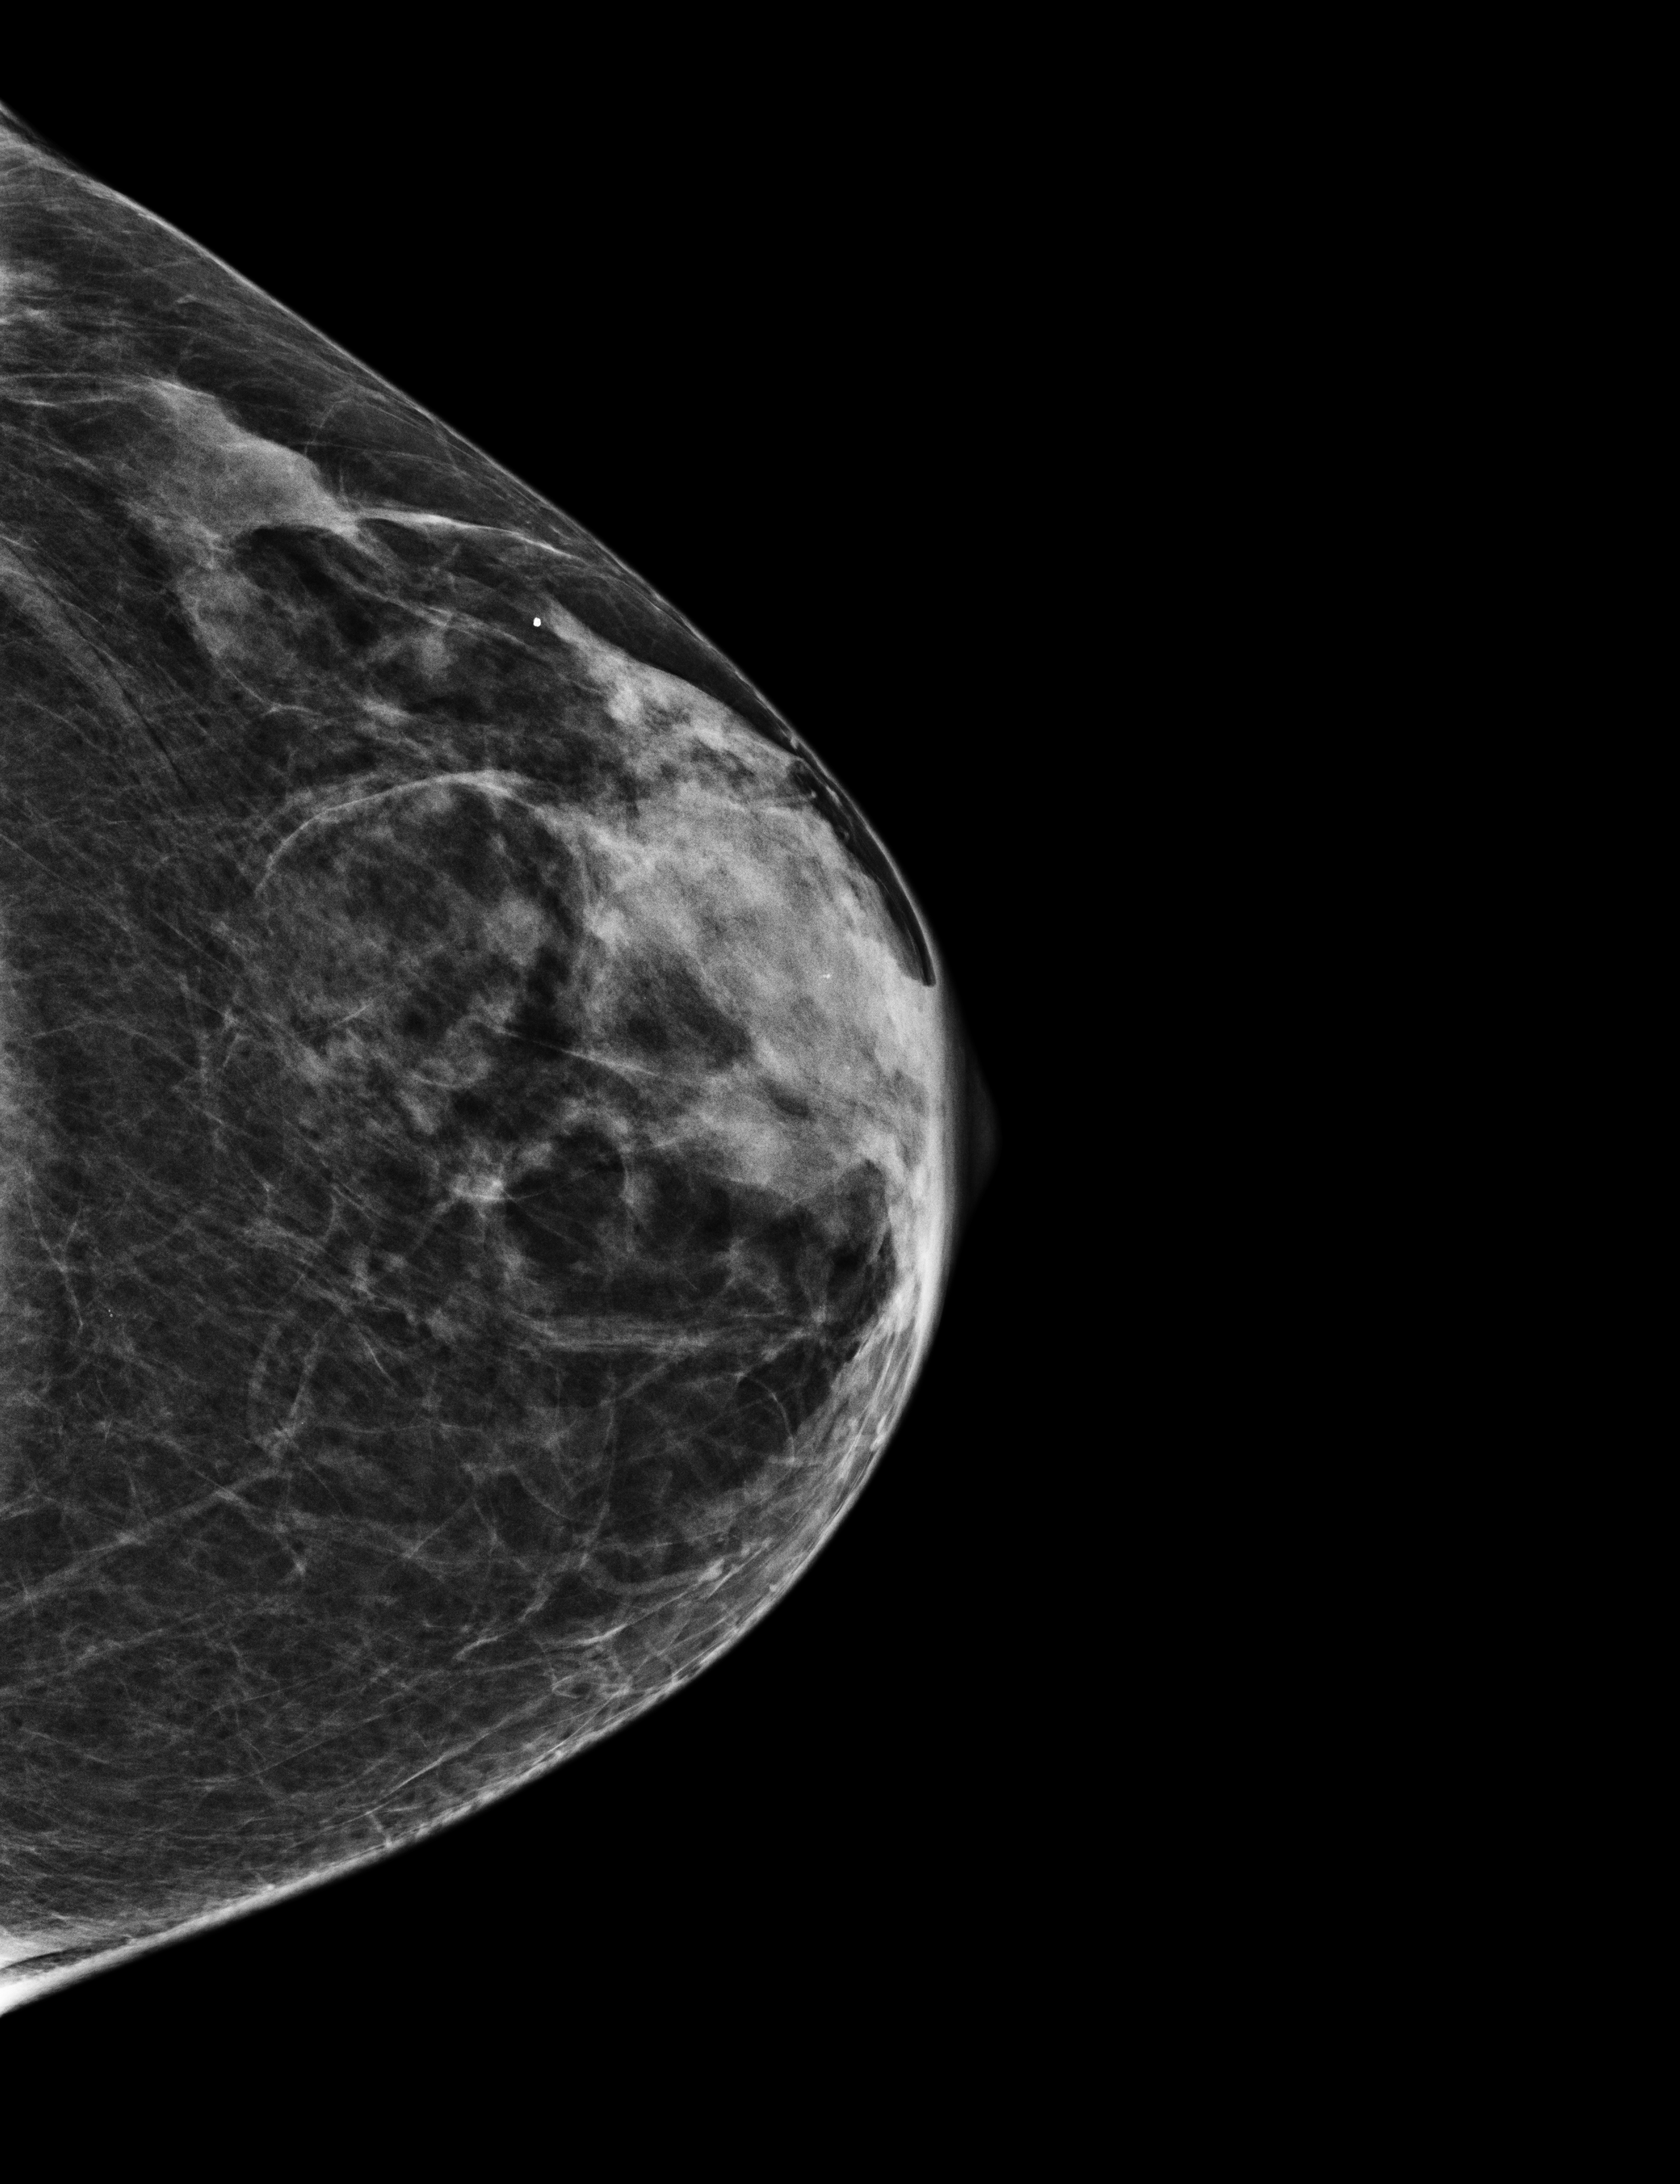
Diagnostic examination (additional views); system: Selenia Dimensions.
Image type: full-field digital mammogram. Breast: left. Projection: CC view.